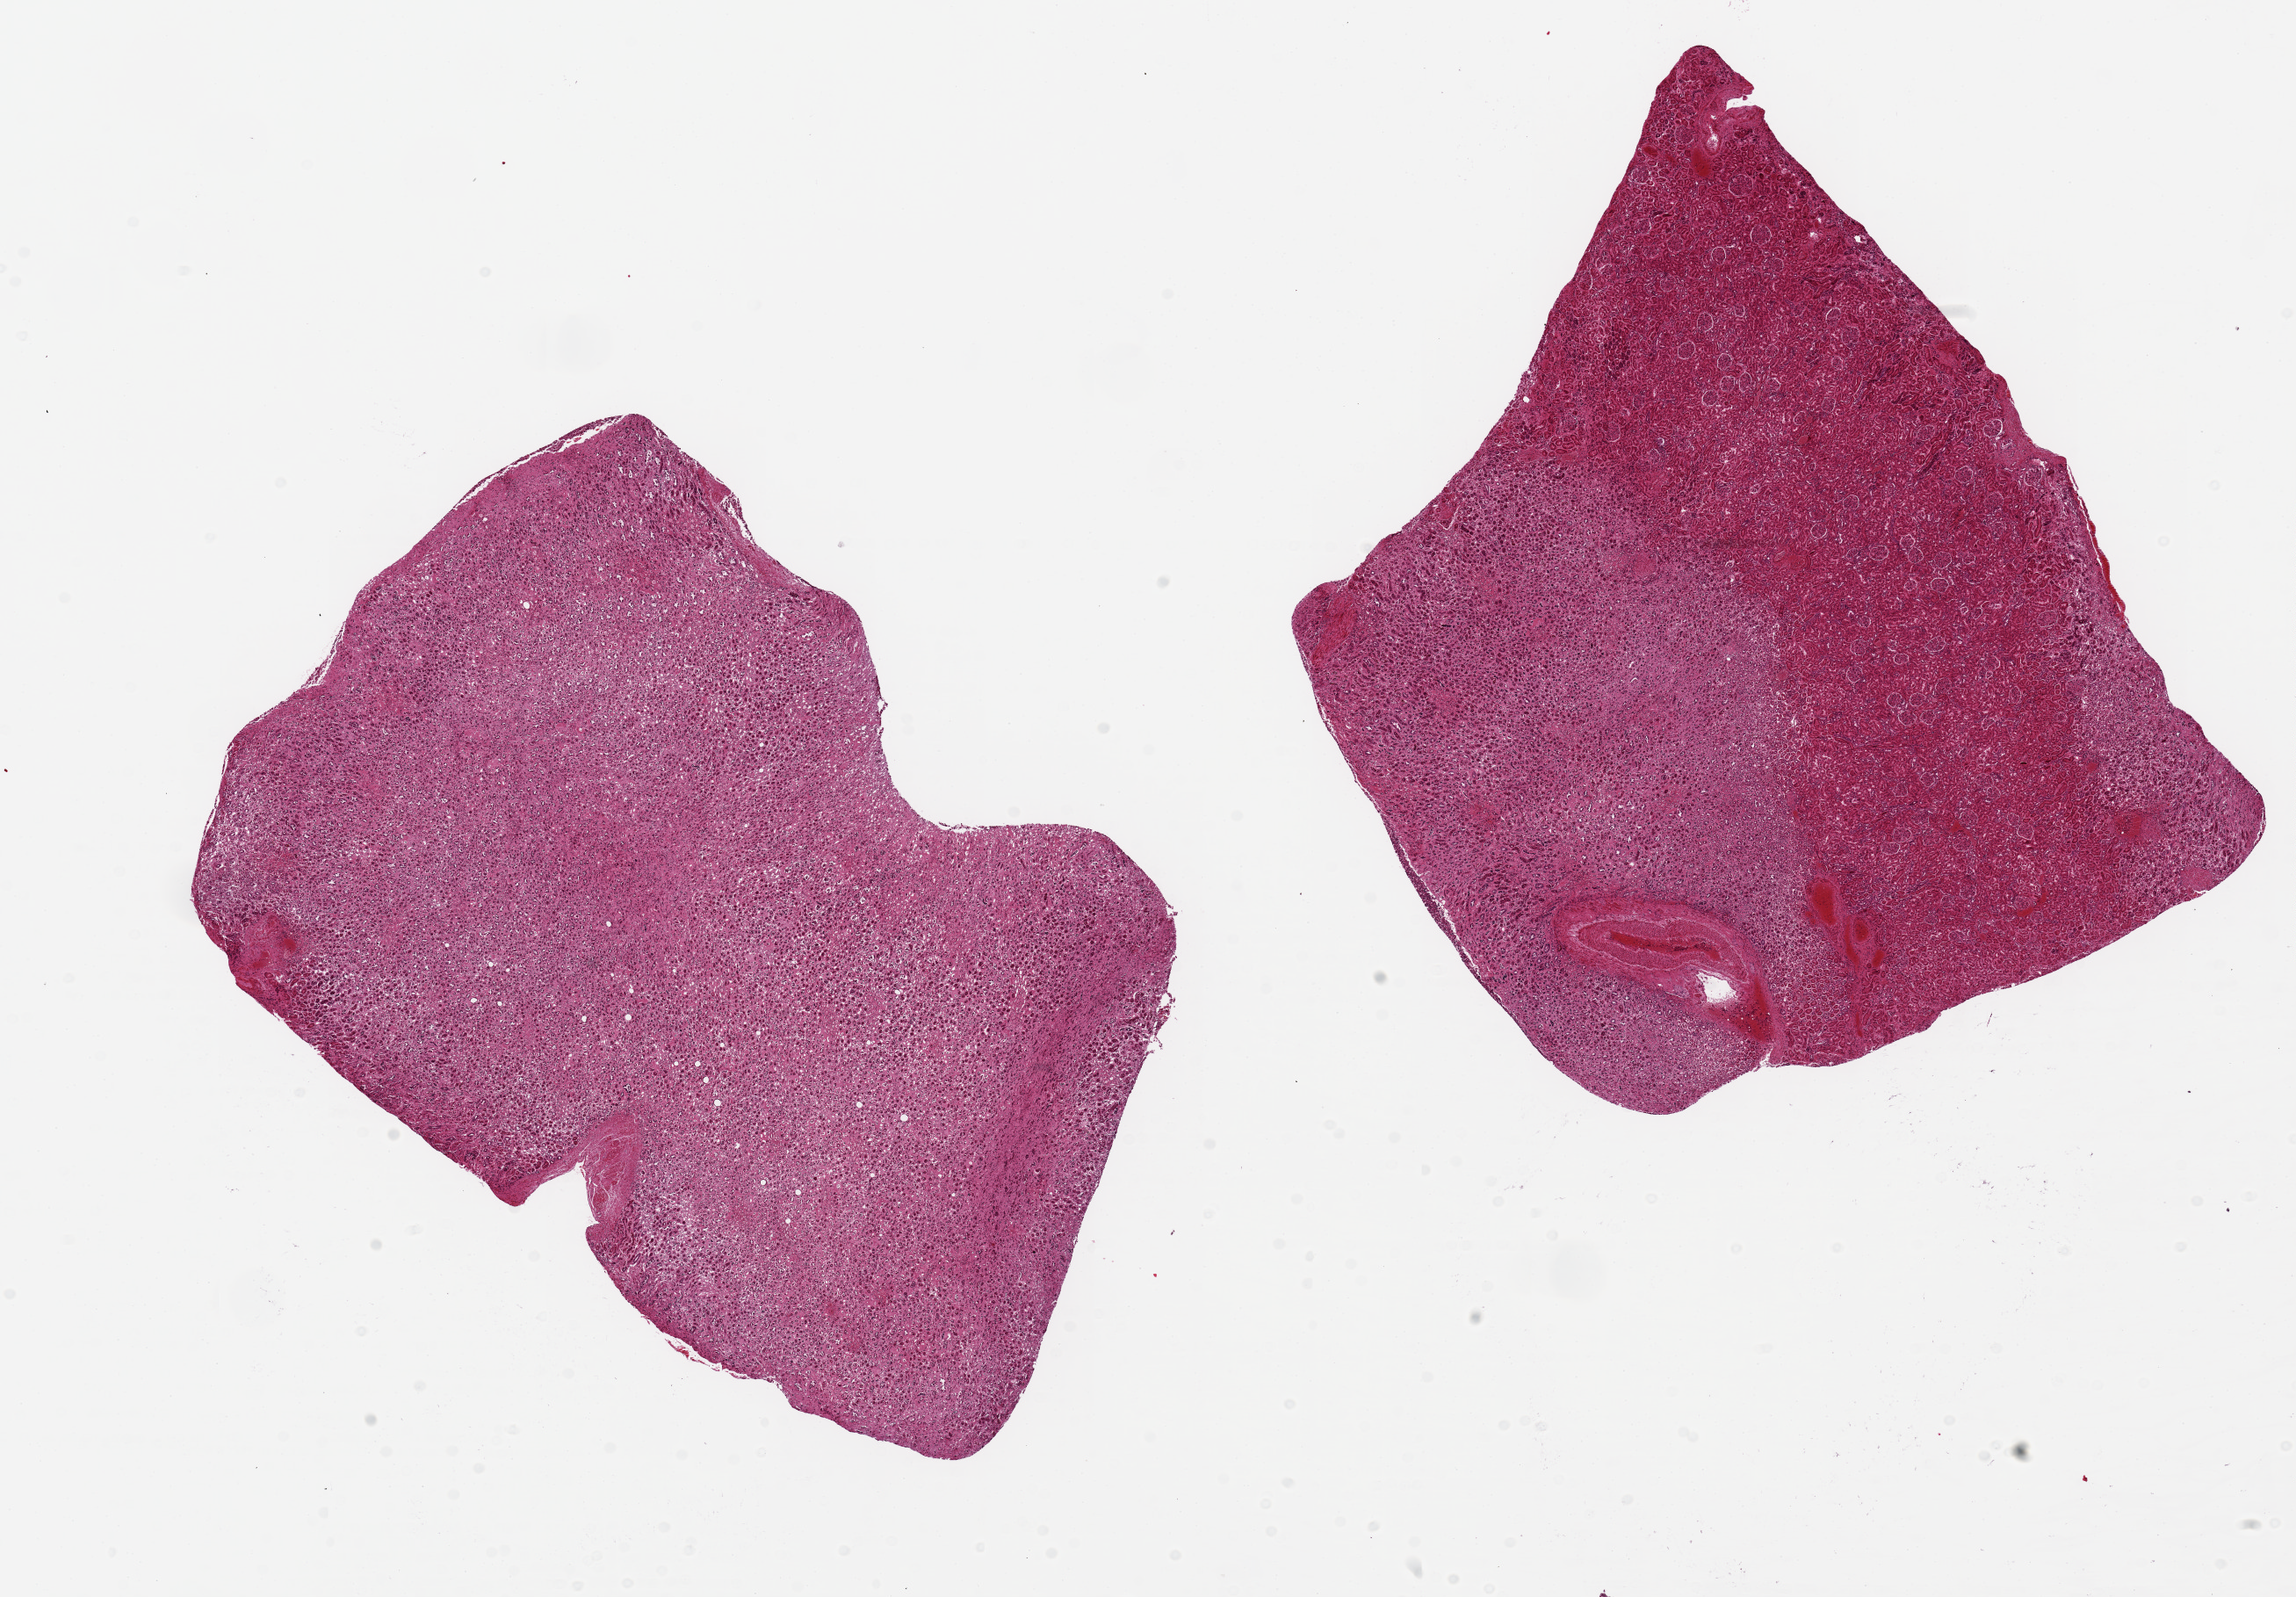
Digitized H&E-stained section — low-resolution overview of the scanned area, about 20.7 x 14.4 mm (acquisition: 20x scan). Donor: male.
Specimen: PAXgene-fixed, paraffin-embedded tissue; target tissue: renal medulla; donor tissue sample.